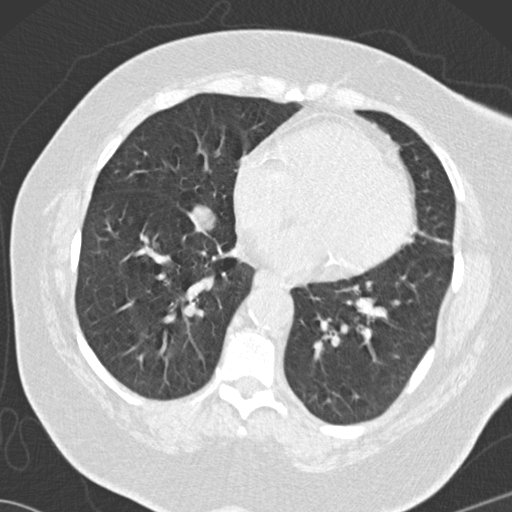
Low-dose screening chest CT, one axial slice. Slice 54 of 146 in the series (ordered by position). Reconstruction kernel B30f. 120 kVp. Lung window (W 1500 / L -600 HU). 2 mm slice thickness. 512 × 512 image matrix.
Annotated regions visible in this slice (manually delineated by an expert):
- lesion 3 (tumor, lower lobe of right lung): bounding box (x1, y1, x2, y2) in pixels: (193, 206, 216, 231)